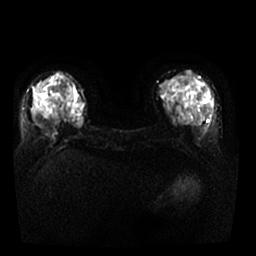
Breast MRI, one axial slice. Slice 12 of 29 in the series (ordered by position). Diffusion-weighted series; image 2 of 4 stored at this slice position (different b-values; order by instance number). 1.5 T. 256 × 256 image matrix. Female patient.
Annotated regions visible in this slice (expert manual segmentation):
- tumour on diffusion-weighted imaging: bounding box [x1, y1, x2, y2] px = [76, 118, 83, 126]